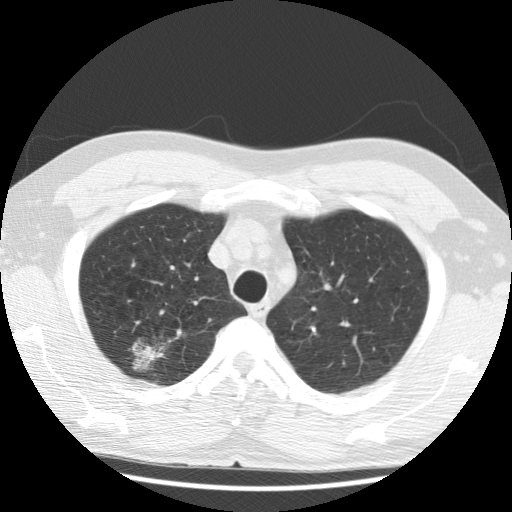
Low-dose screening chest CT, axial slice. First (baseline) screen. Lung window (W 1500 / L -600 HU). 2.5 mm slice thickness. Slice 27 of 122 in the series. 512 × 512 image matrix. Male, age 59 years at enrolment. Former smoker at enrolment.
Expert-annotated lung lesion, bounding box [x1, y1, x2, y2] px = [112, 325, 178, 387]. Screening reader's record for this exam (one nodule recorded; not confirmed to be the boxed lesion): non-calcified nodule or mass ≥4 mm, right upper lobe, 30 × 28 mm, poorly defined margins, ground glass attenuation. Later outcome: lung cancer diagnosed 40 days after this screen — bronchiolo-alveolar carcinoma, non-mucinous, right upper lobe, well differentiated (G1), stage IA (AJCC 6th edition), 15 mm at pathology.